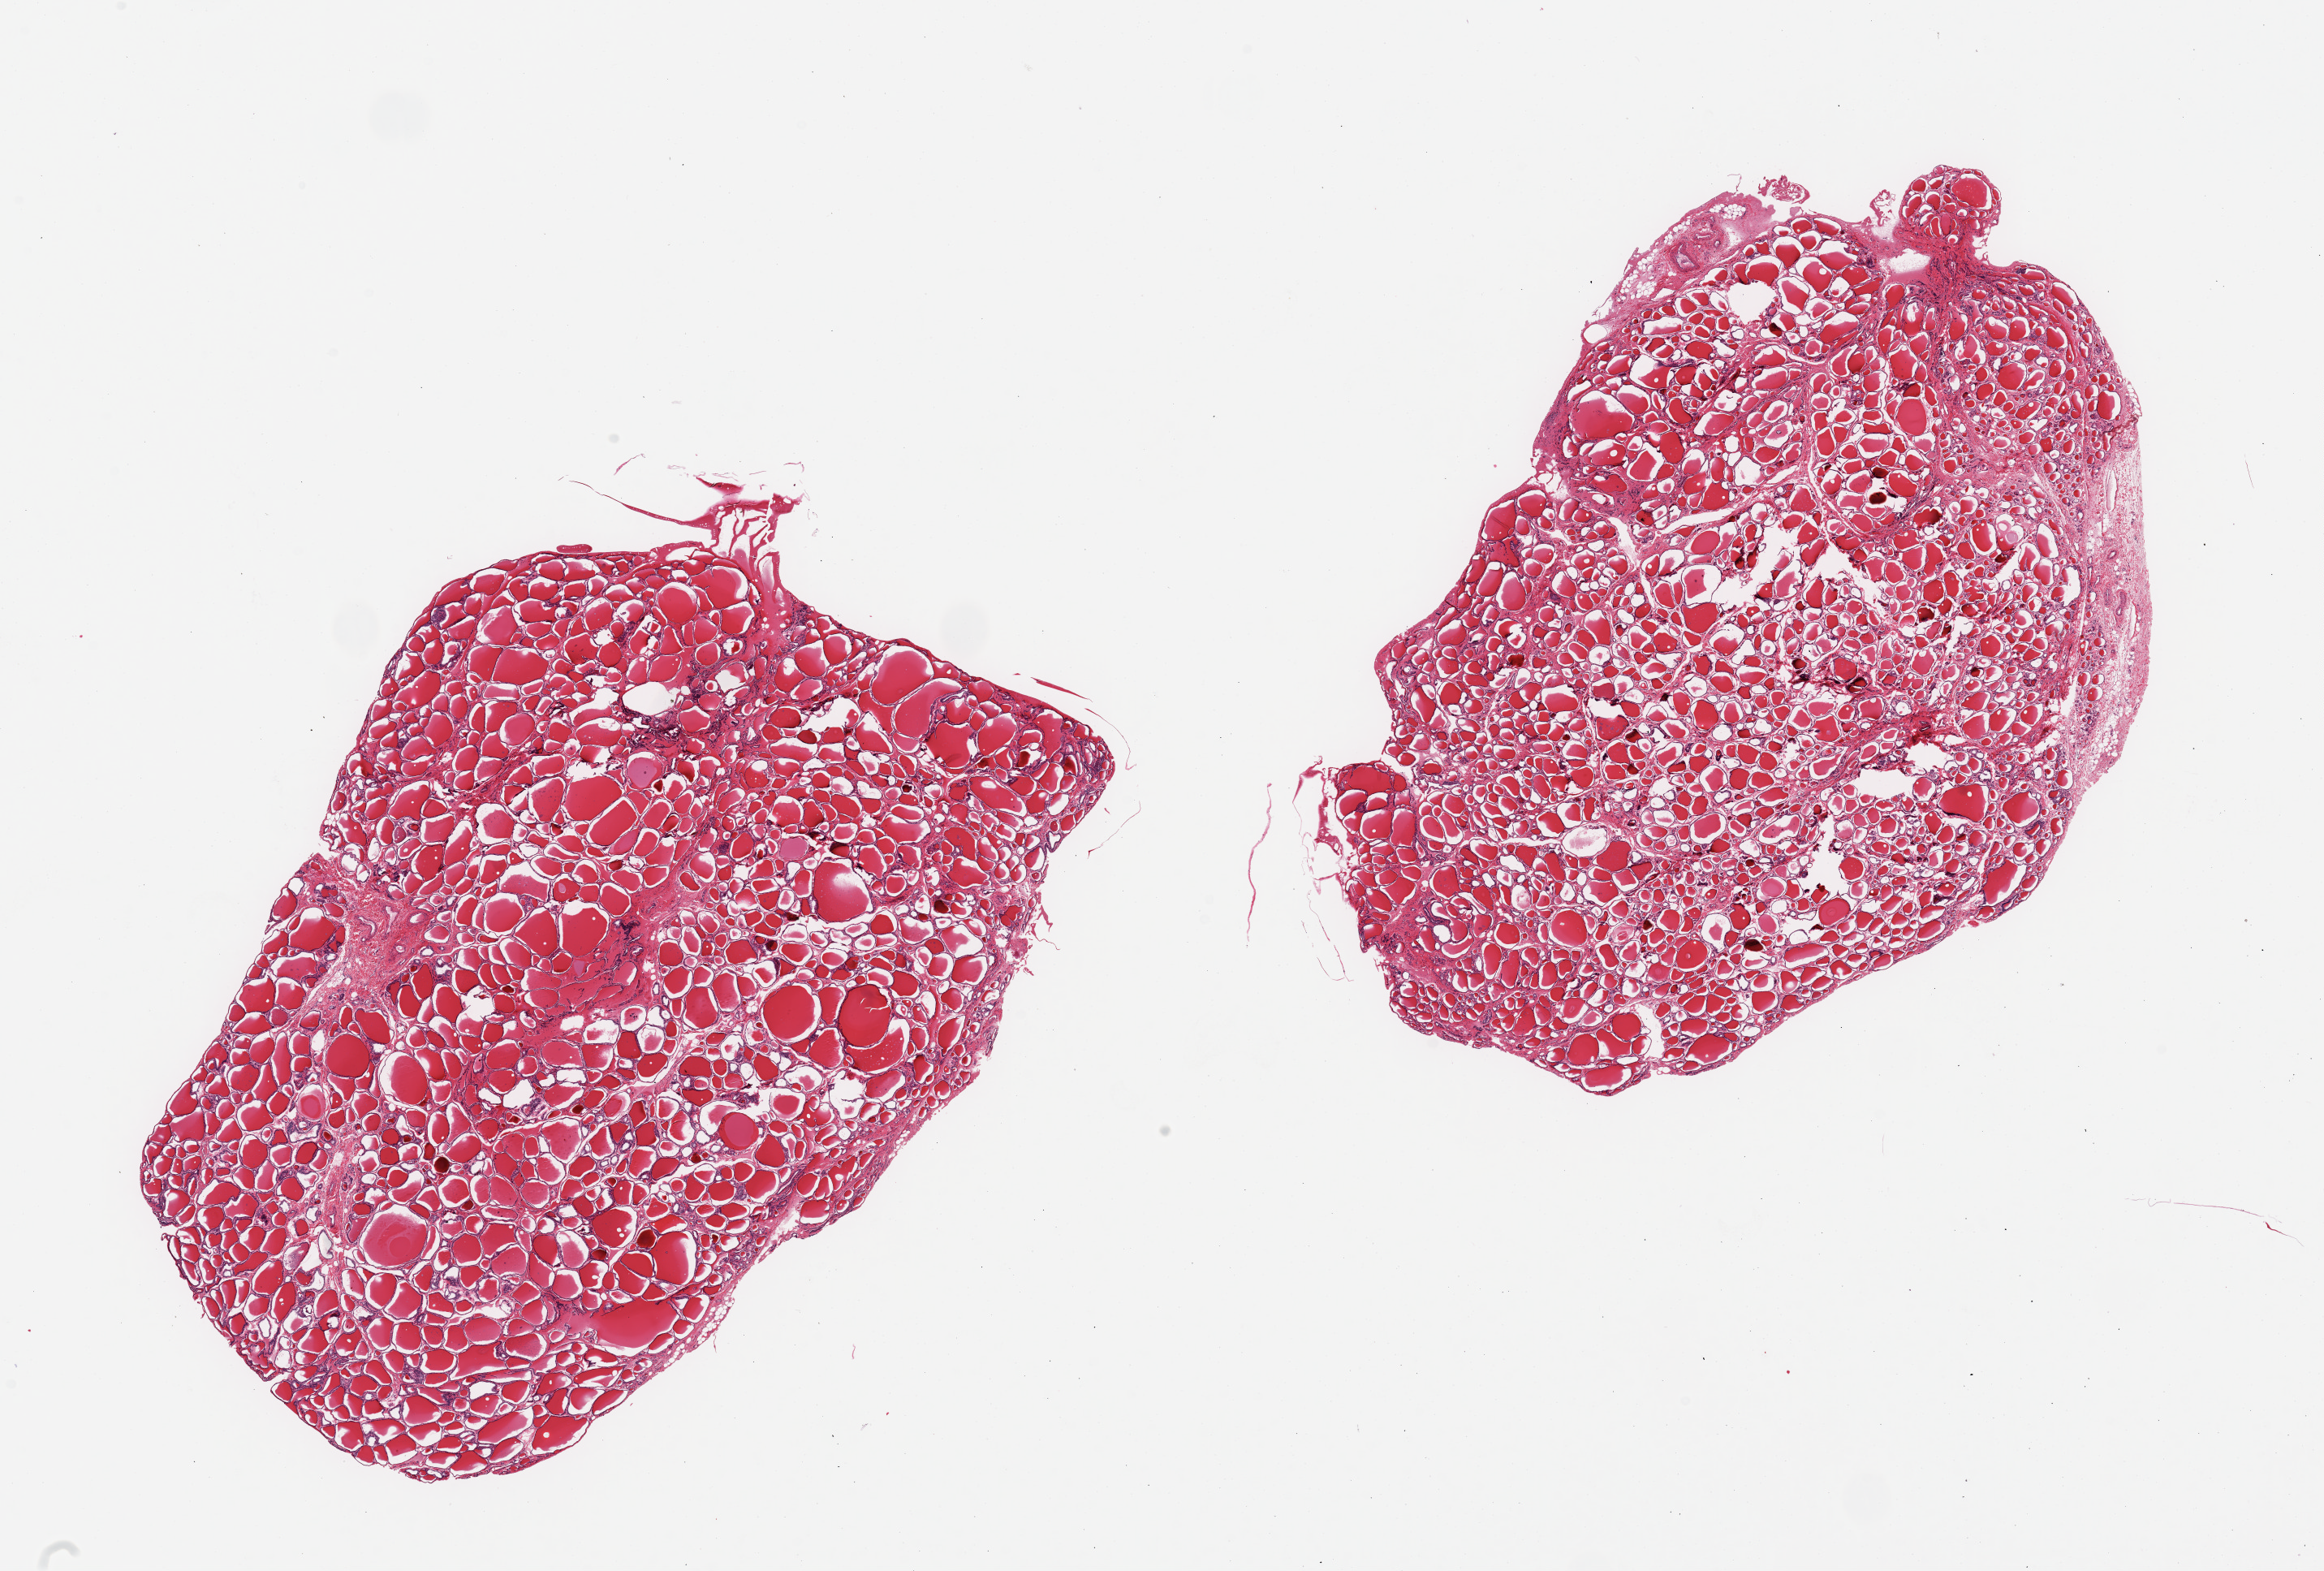
Digitized H&E-stained section, low-resolution overview of the scanned area, about 22.6 x 15.3 mm; PAXgene-fixed paraffin-embedded (PFPE) section; sampled site (target tissue): thyroid; donor tissue sample. Donor: male.
Review note (as recorded): 2 pieces; 1 piece includes small attachment of fat/vessels.